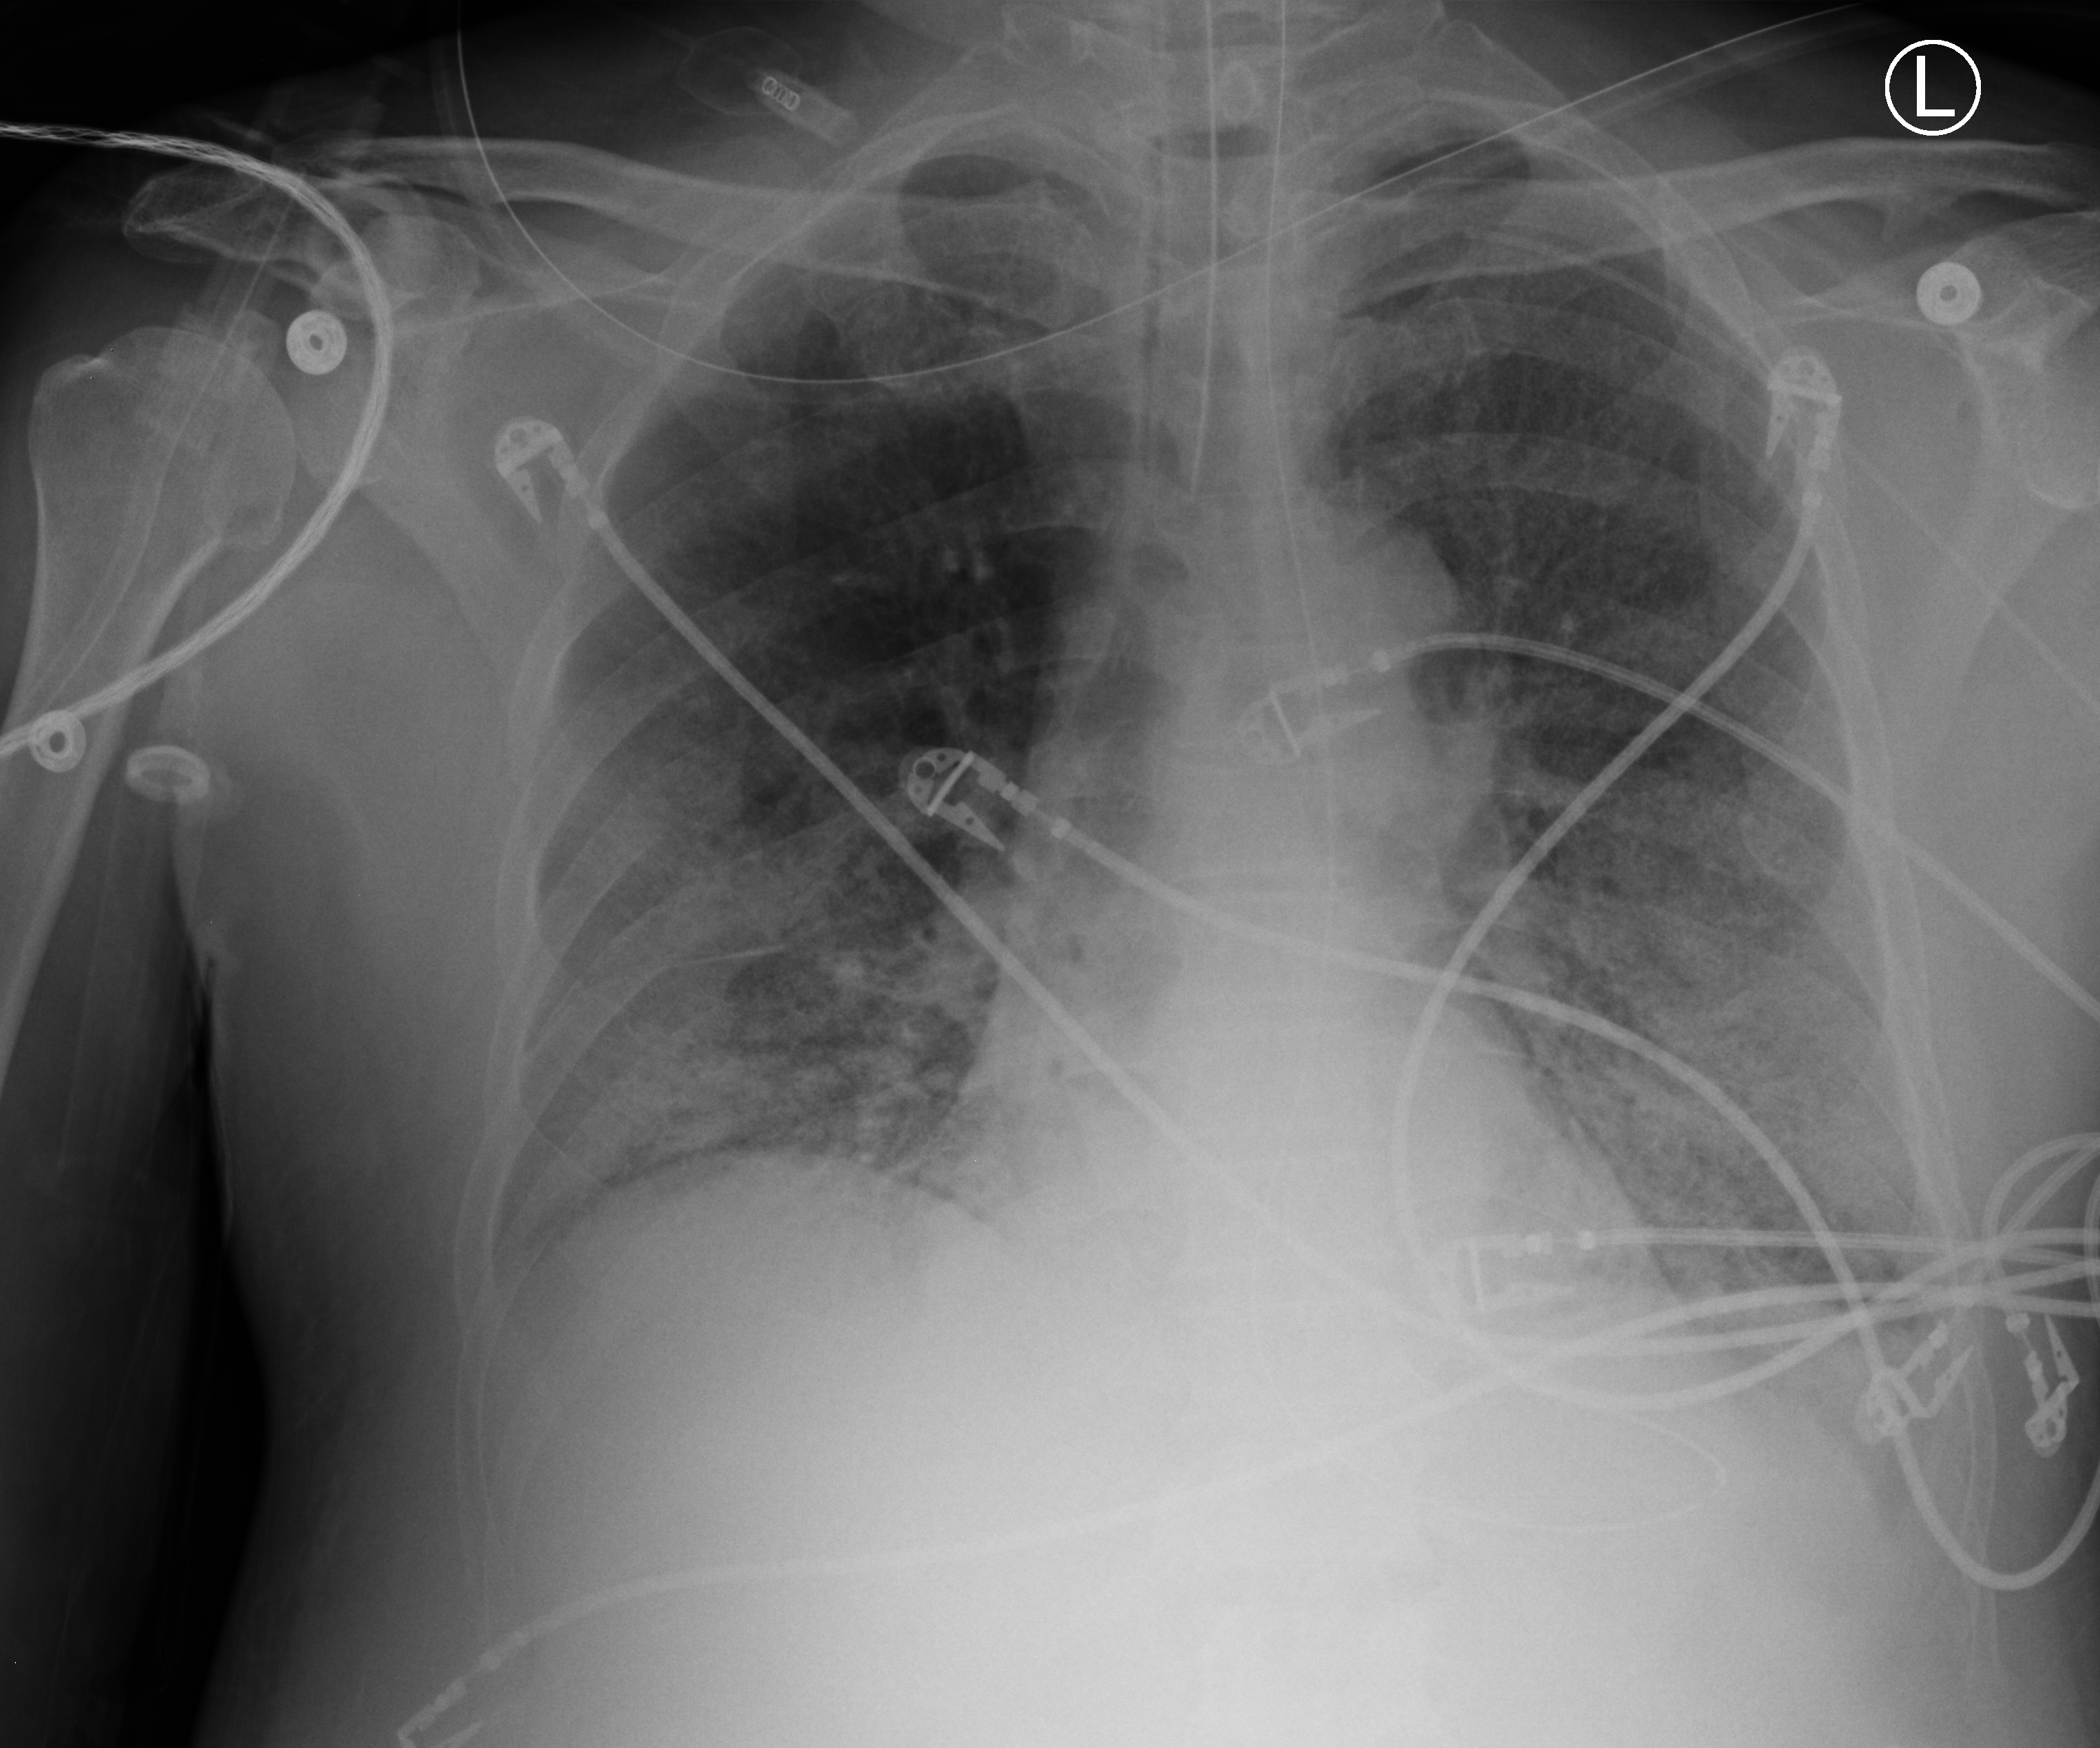
Portable chest radiograph, anteroposterior (AP) projection. Male patient hospitalised with COVID-19, age 60–74 years.
Hospital-stay facts (about this admission, not read from this image; timing relative to this image not recorded):
- admitted to intensive care during this hospital stay: yes
- mechanically ventilated during this hospital stay: yes